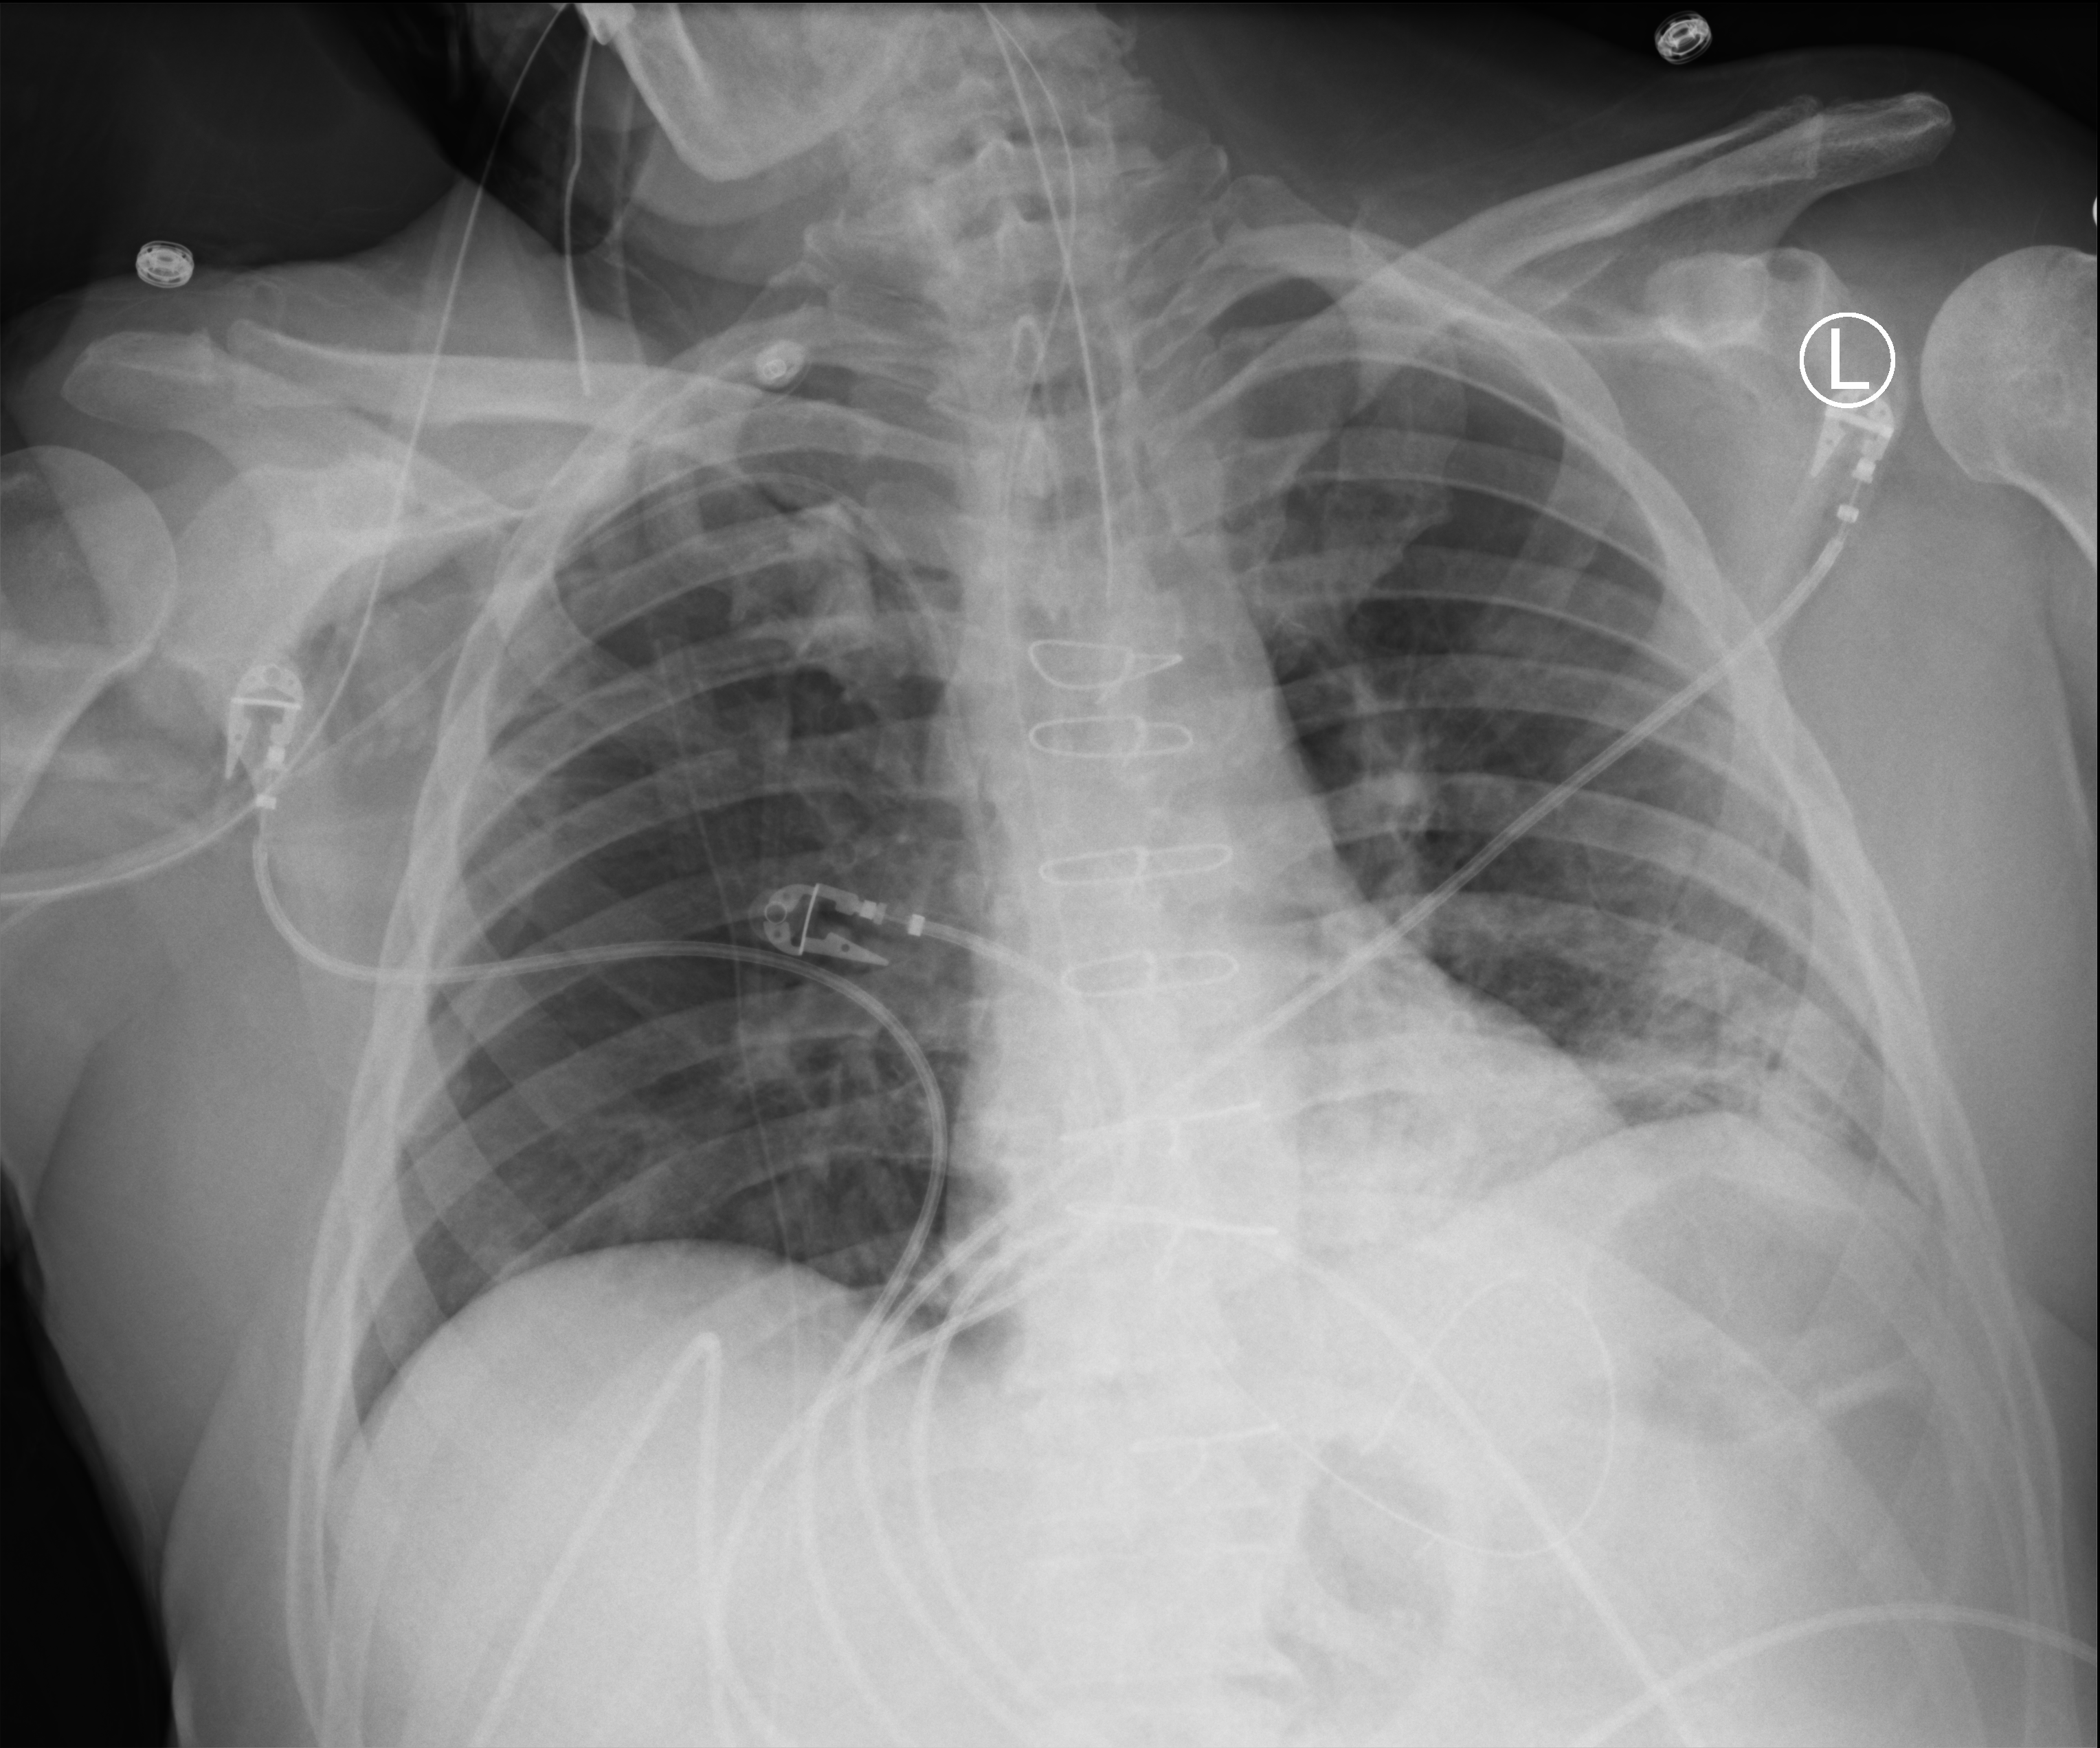
Chest X-ray (portable); anteroposterior (AP) projection. Patient hospitalised with COVID-19; male, aged 60–74 years.
Admission-level facts for this patient (not findings on this image; timing relative to this image not recorded): admitted to intensive care during this hospital stay: yes; hypertension (admission record): yes.